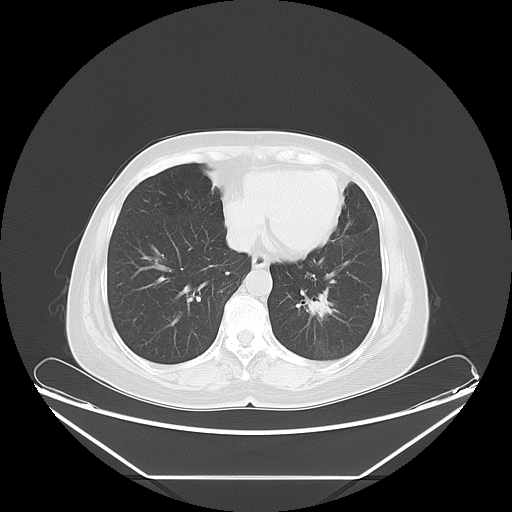
Chest CT, one axial slice; reconstruction kernel LUNG; 120 kVp; lung window (W 1500 / L -600 HU); 5 mm slice thickness; 512 × 512 image matrix, field of view 451 × 451 mm. Patient: female, 63 years. Case-level facts recorded for this patient, not image findings: clinical TNM (as recorded): T1c N0 M0.
Annotated regions visible in this slice (rectangle marked by the reading radiologist):
- lung tumour (recorded histology: adenocarcinoma): bounding box <302,286,337,322> (left, top, right, bottom; pixels)